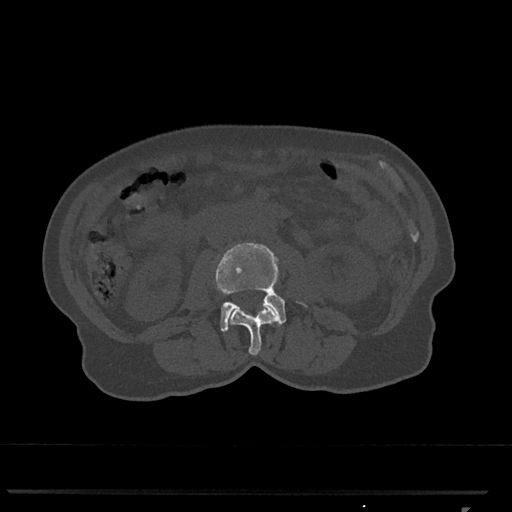
CT including the spine, one axial slice; slice 300 of 793 in the series (ordered by position); reconstruction kernel Br40s/3; bone window (W 1800 / L 400 HU); 0.5 mm slice thickness; 512 × 512 image matrix, field of view 380 × 380 mm. Patient: female, 62 years. Case-level facts recorded for this patient, not image findings: primary cancer: renal.
Annotated regions visible in this slice (semi-automatic segmentation, software-assisted and operator-edited):
- L2 vertebra: box from (x=228, y=305) to (x=278, y=356) px
- L3 vertebra: (x=216, y=242)–(x=307, y=332)